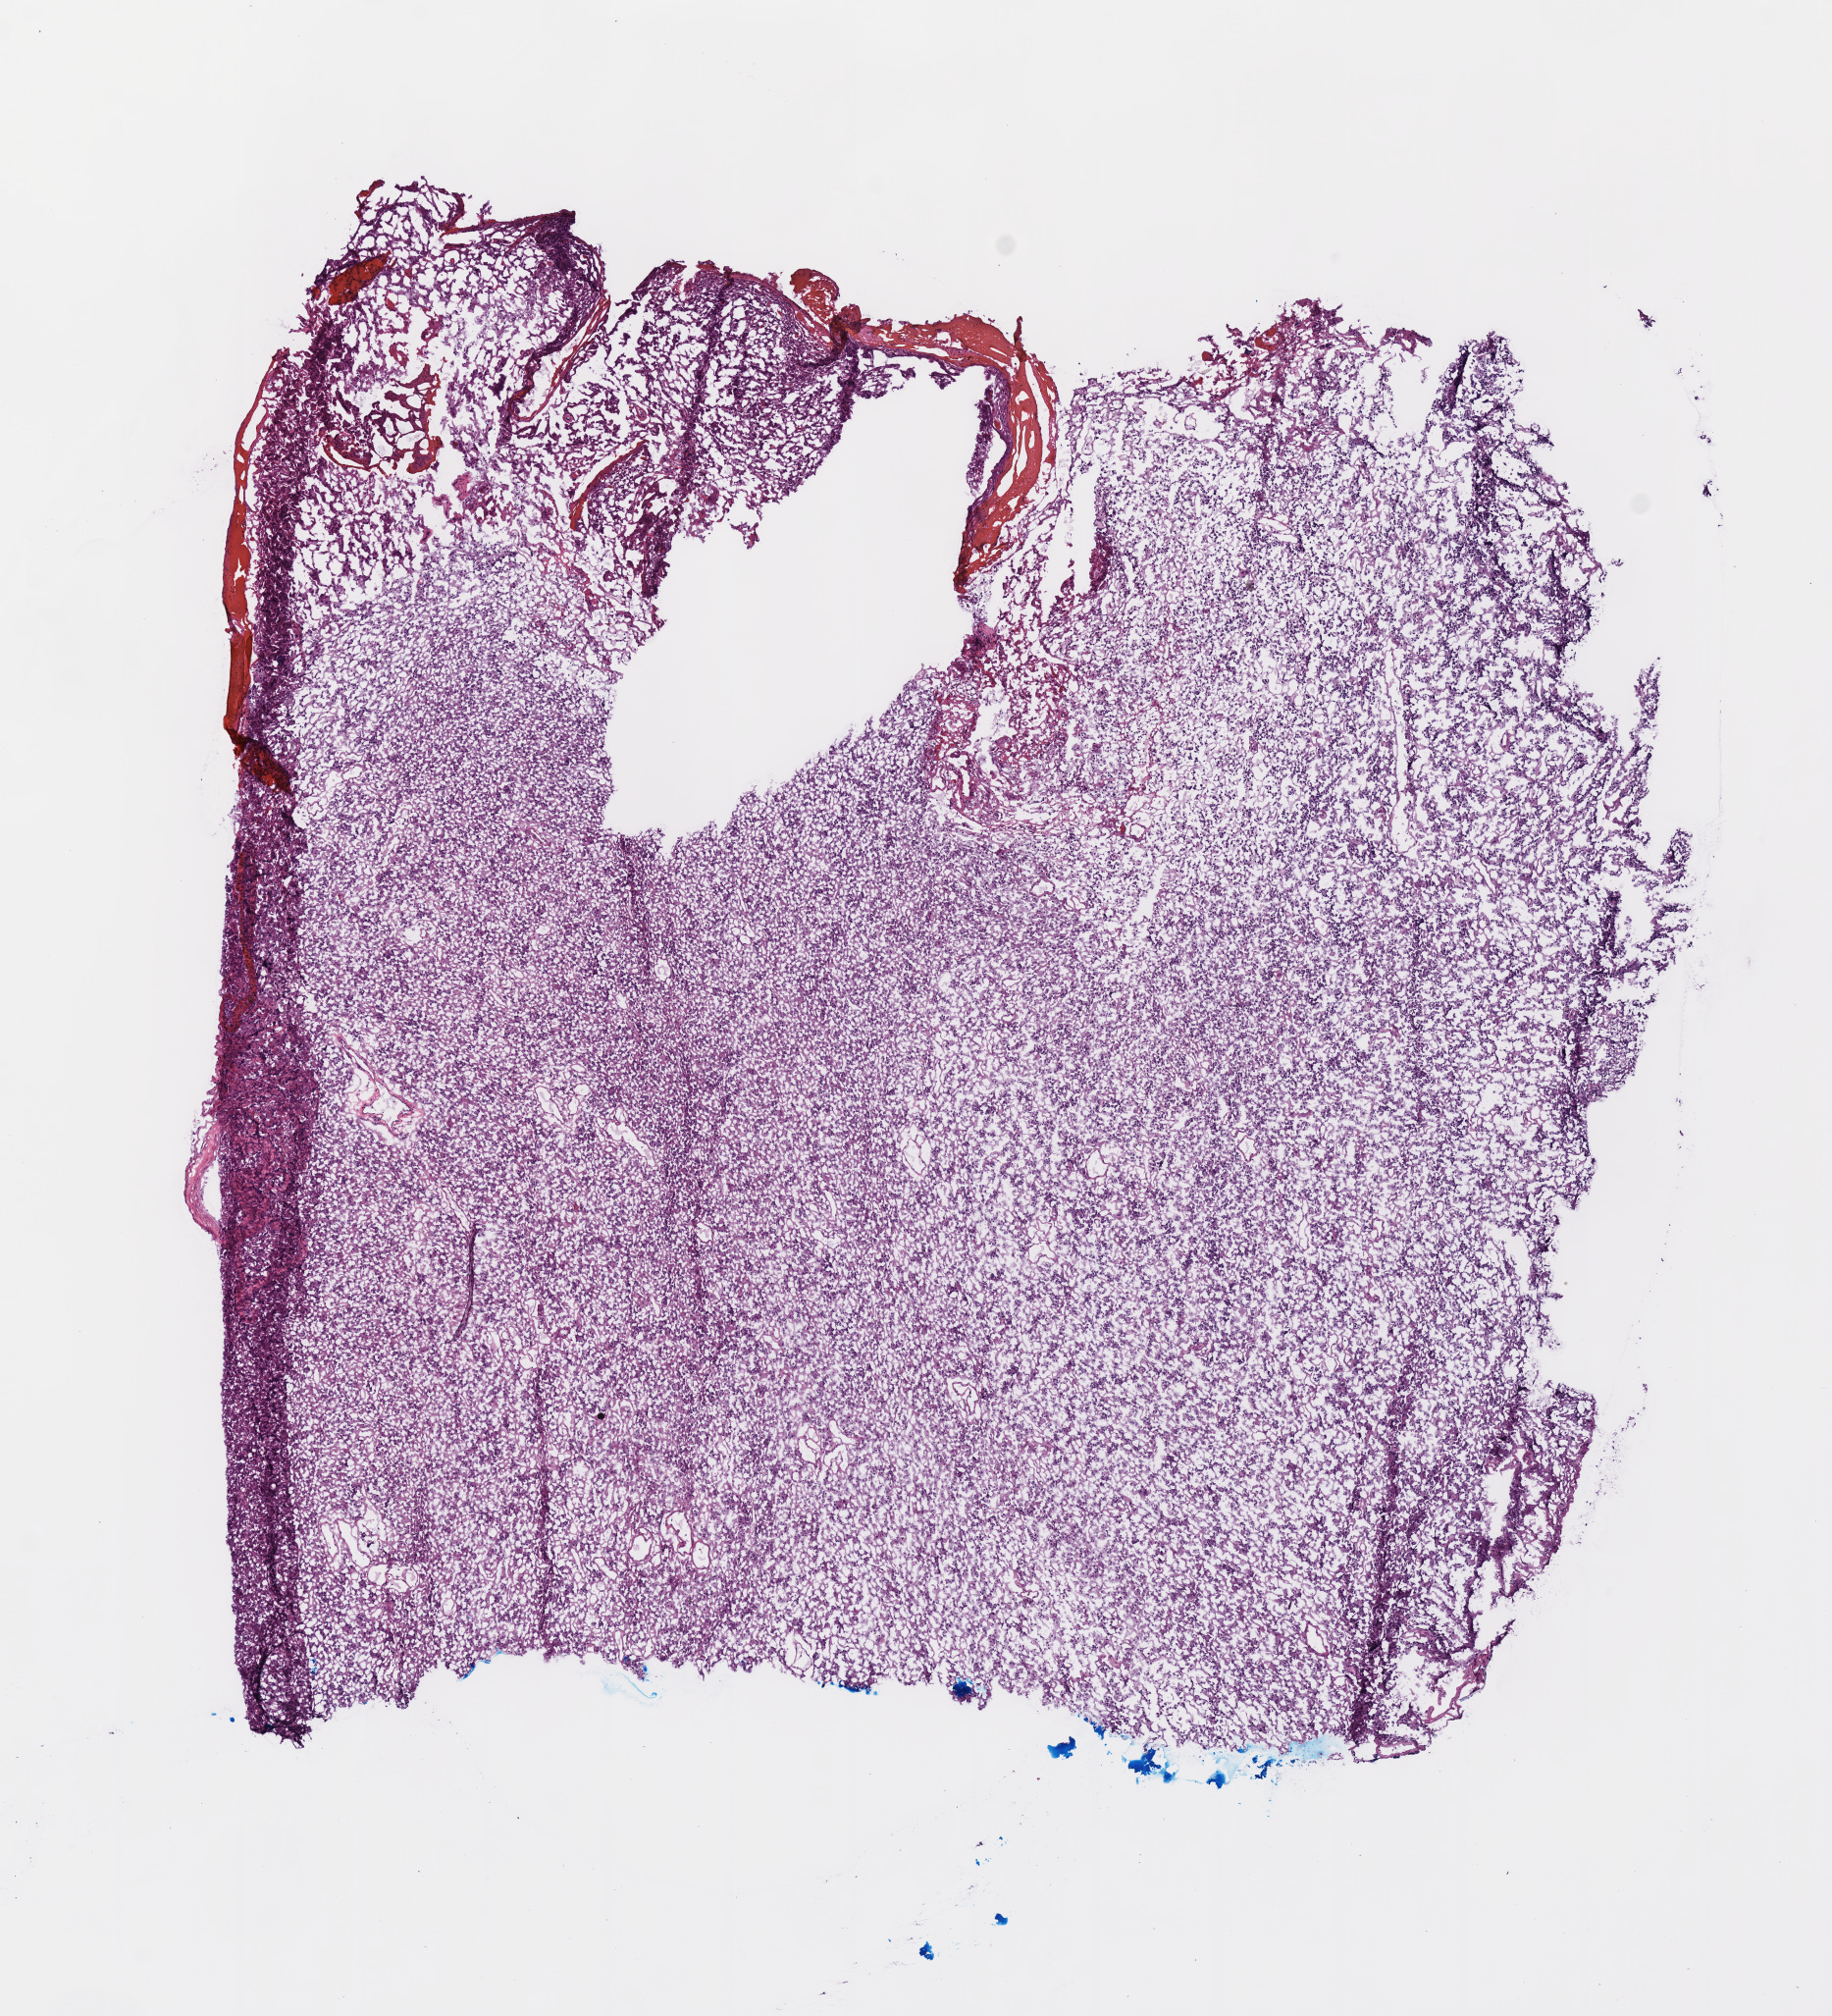
Digitized H&E tissue section (whole slide) — whole scanned area (about 7.3 x 8.1 mm, slide scanned at 40x) shown as a low-resolution overview; frozen section; sample: primary tumour, brain. Male, age 49 years at initial diagnosis. Composition of this section per pathologist review: tumour cells 100%, tumour nuclei 80%.
Histologic diagnosis: Mixed glioma.